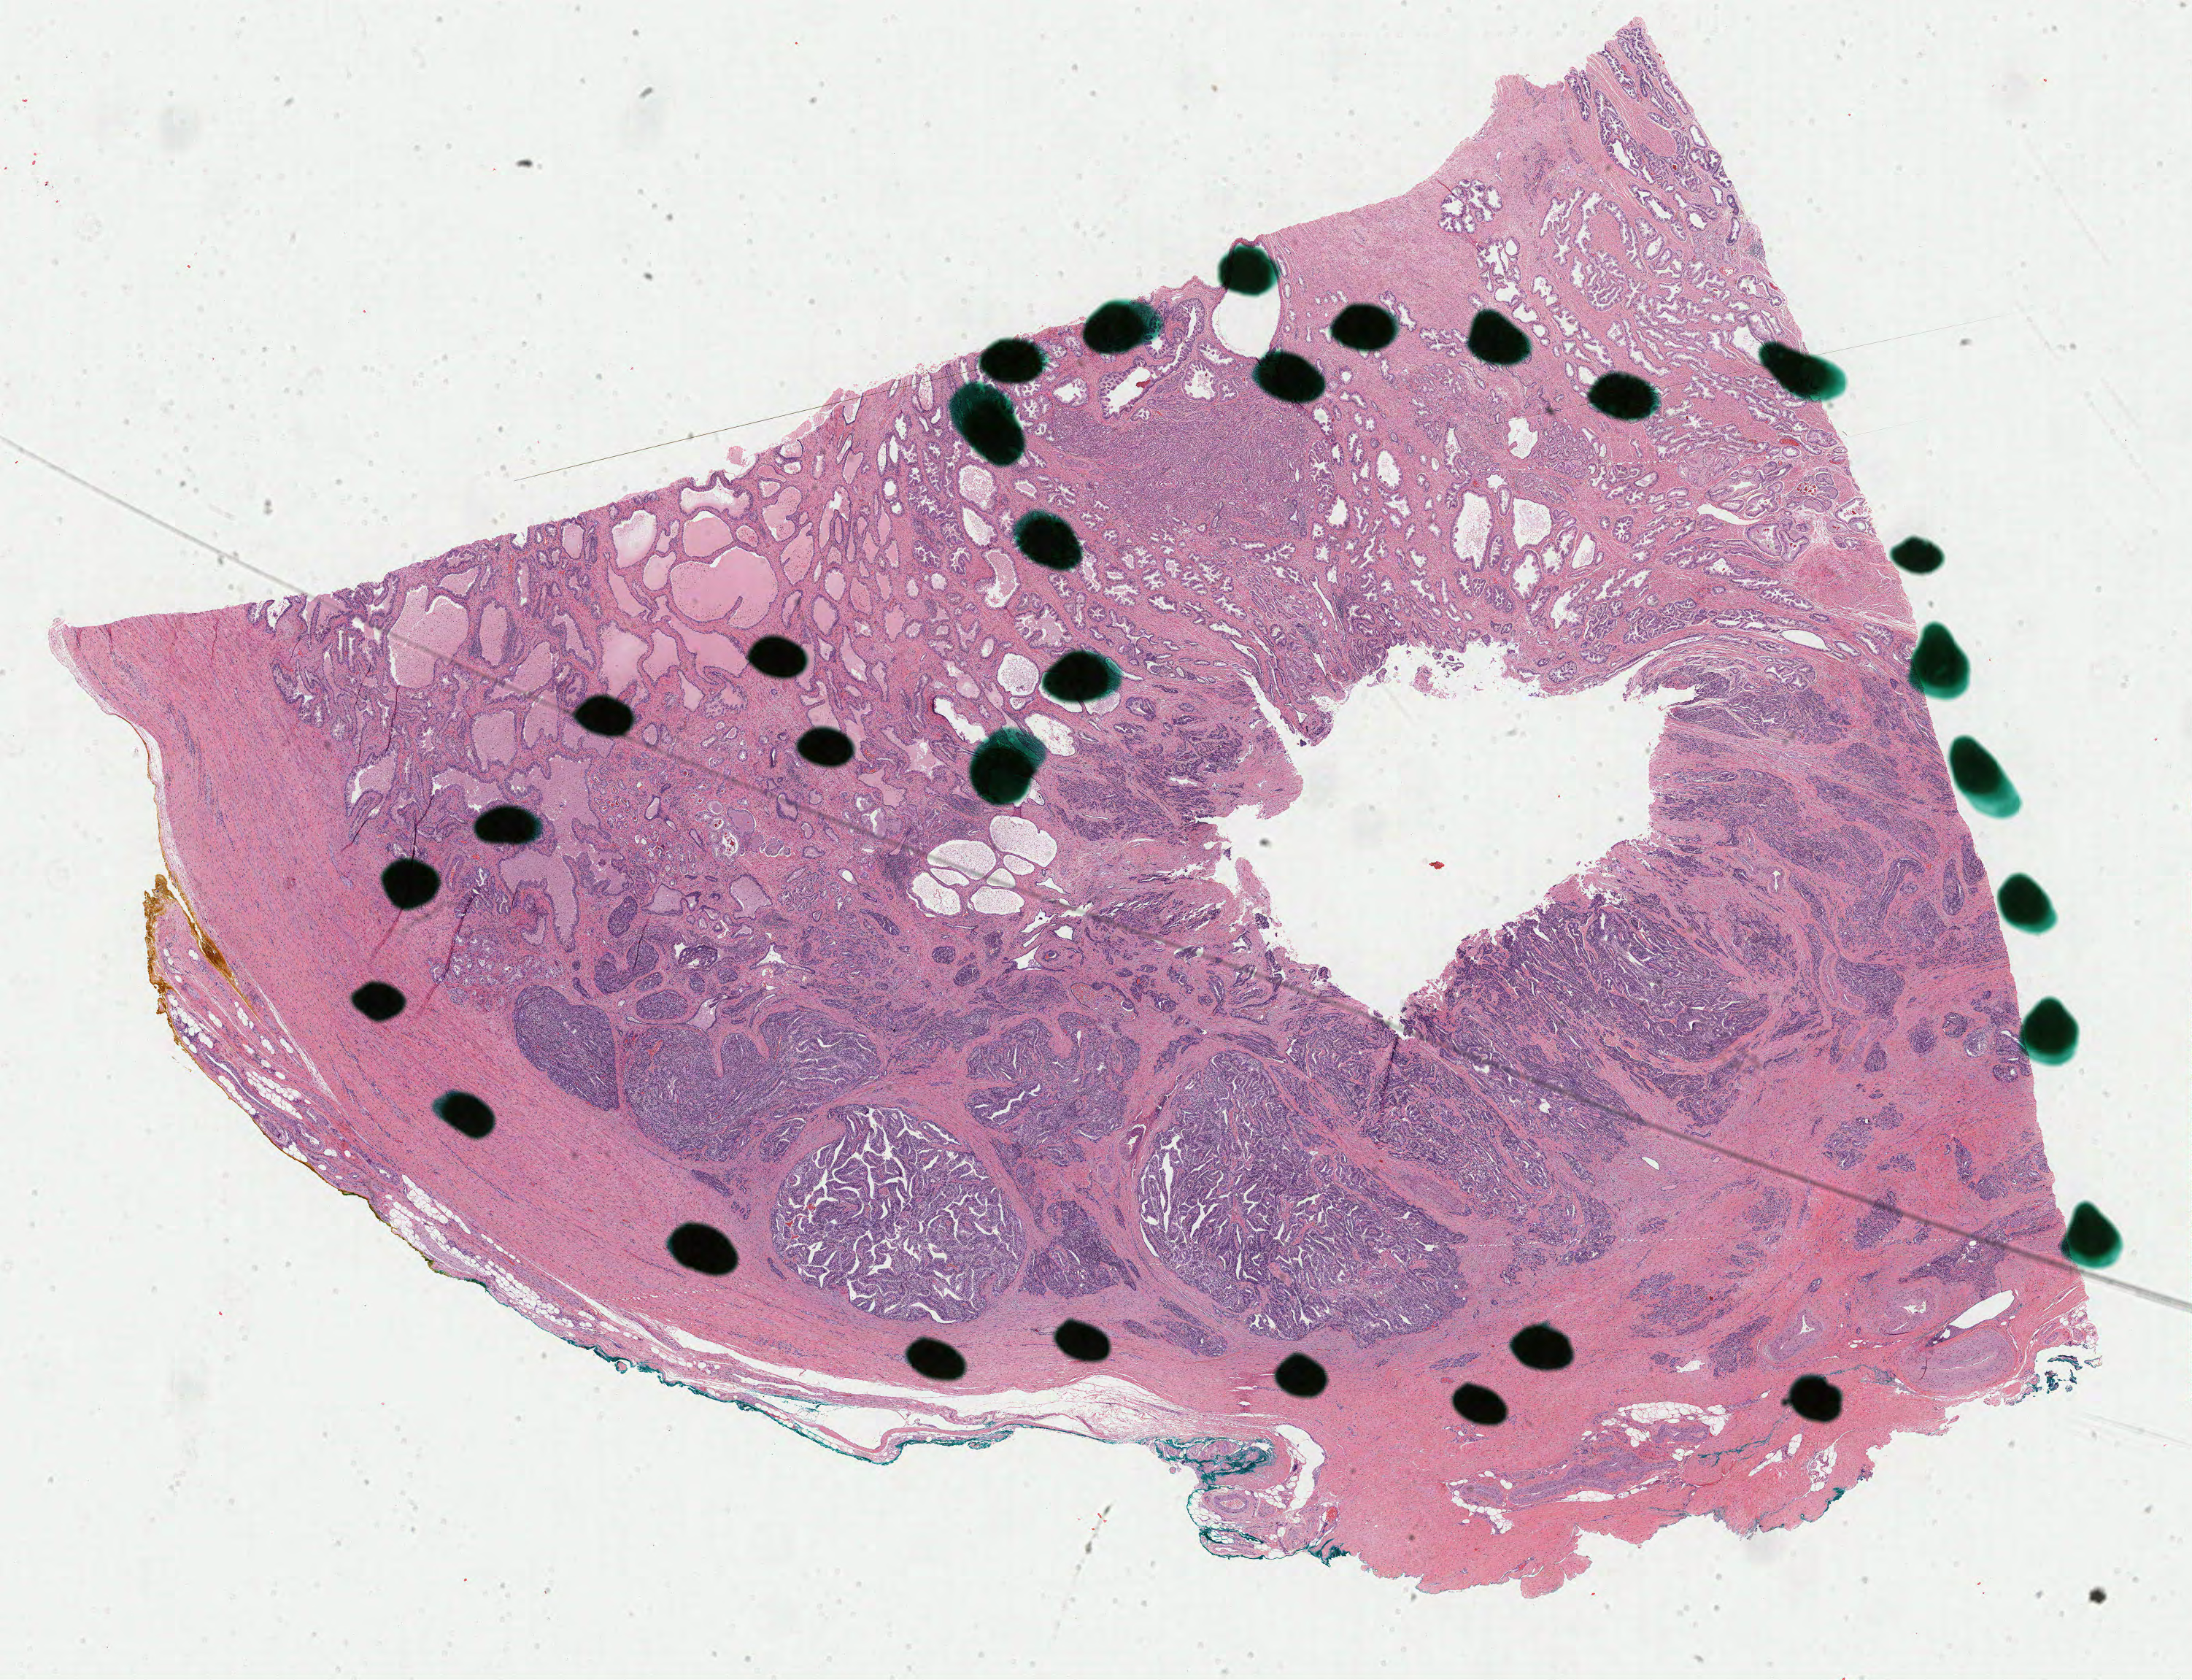
Whole-slide histology image, H&E — whole scanned area (about 23.8 x 18.3 mm) shown as a low-resolution overview, formalin-fixed paraffin-embedded (FFPE) diagnostic section, sample: primary tumour, prostate. Patient: male, age at initial diagnosis 57 years. Gleason score: 7 (4+3).
• diagnosis: Adenocarcinoma, NOS (prostate gland)
• laterality: bilateral